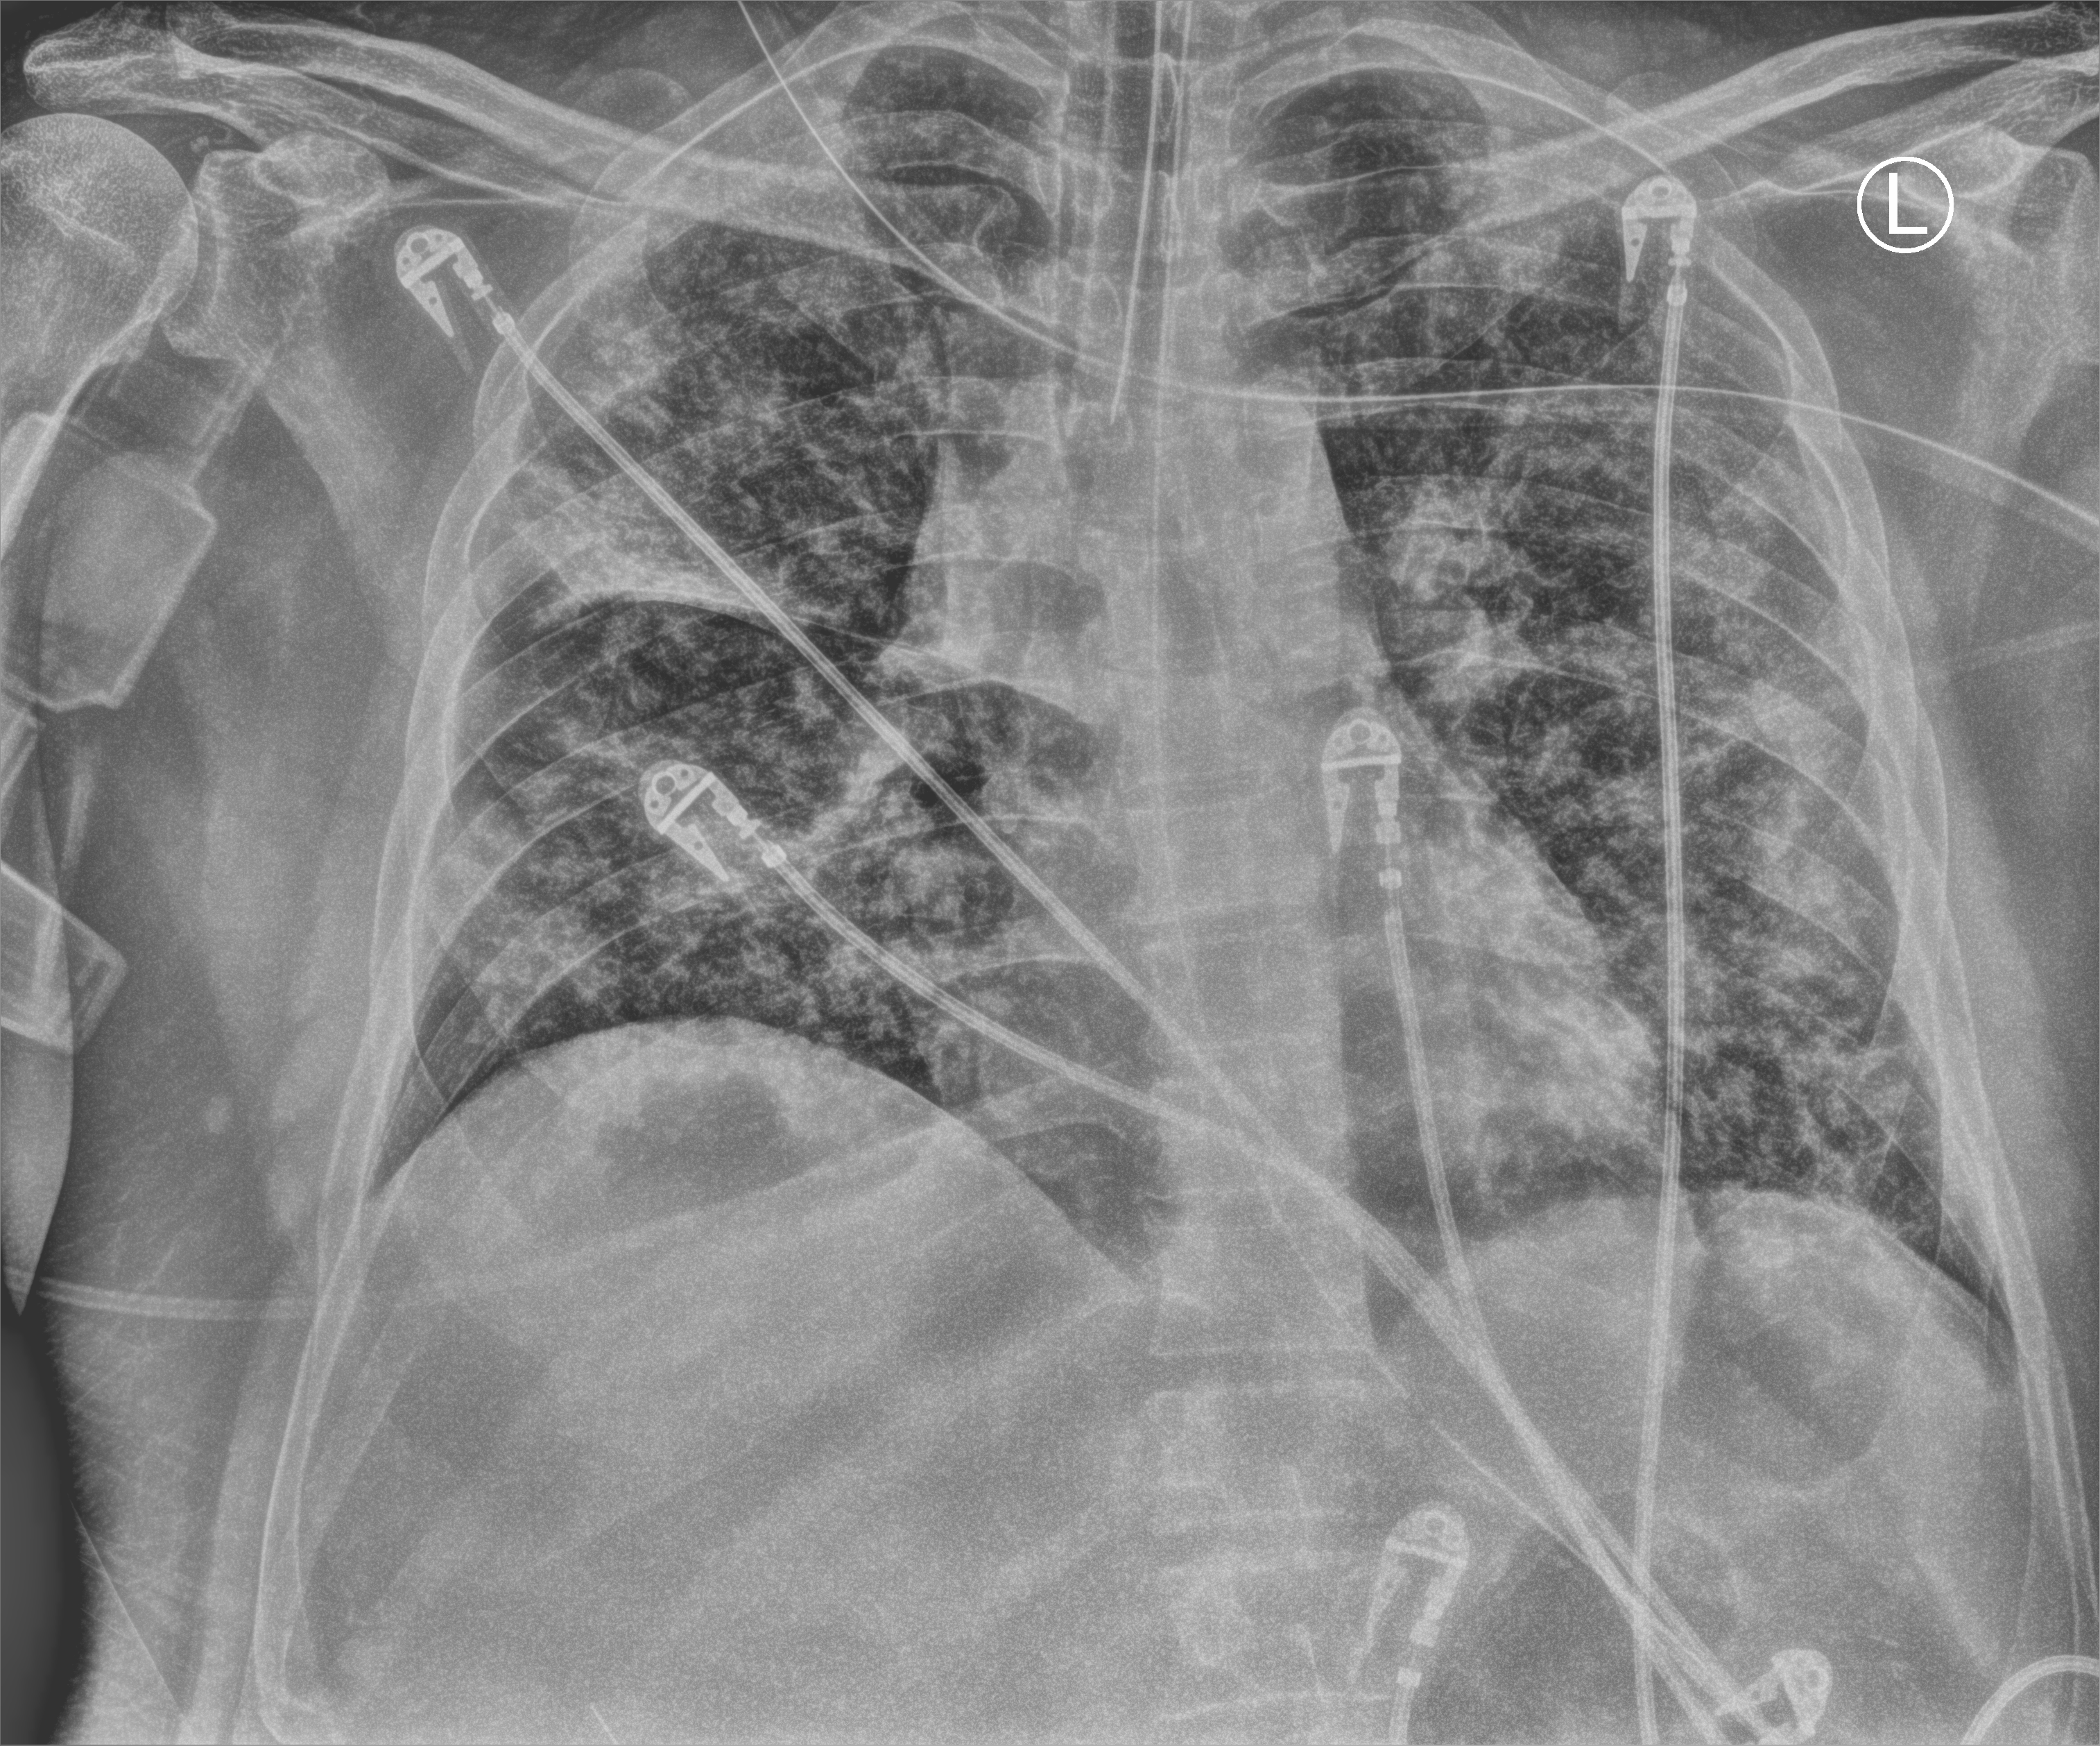
Chest X-ray (portable); anteroposterior (AP) projection. Patient hospitalised with COVID-19, aged 18–59 years.
Admission-level facts for this patient (not findings on this image; timing relative to this image not recorded): mechanically ventilated during this hospital stay: yes.